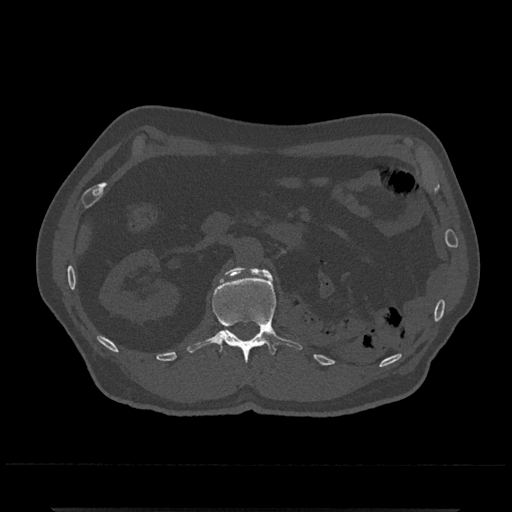
CT including the spine, one axial slice; slice 356 of 797 in the series (ordered by position); reconstruction kernel Br40s/3; 120 kVp; bone window (W 1800 / L 400 HU); 512 × 512 image matrix. Patient: male, 67 years. Case-level facts recorded for this patient, not image findings: primary cancer: prostate.
Outlined on this slice (semi-automatically segmented with operator editing):
- L1 vertebra: box from (x=186, y=266) to (x=302, y=363) px